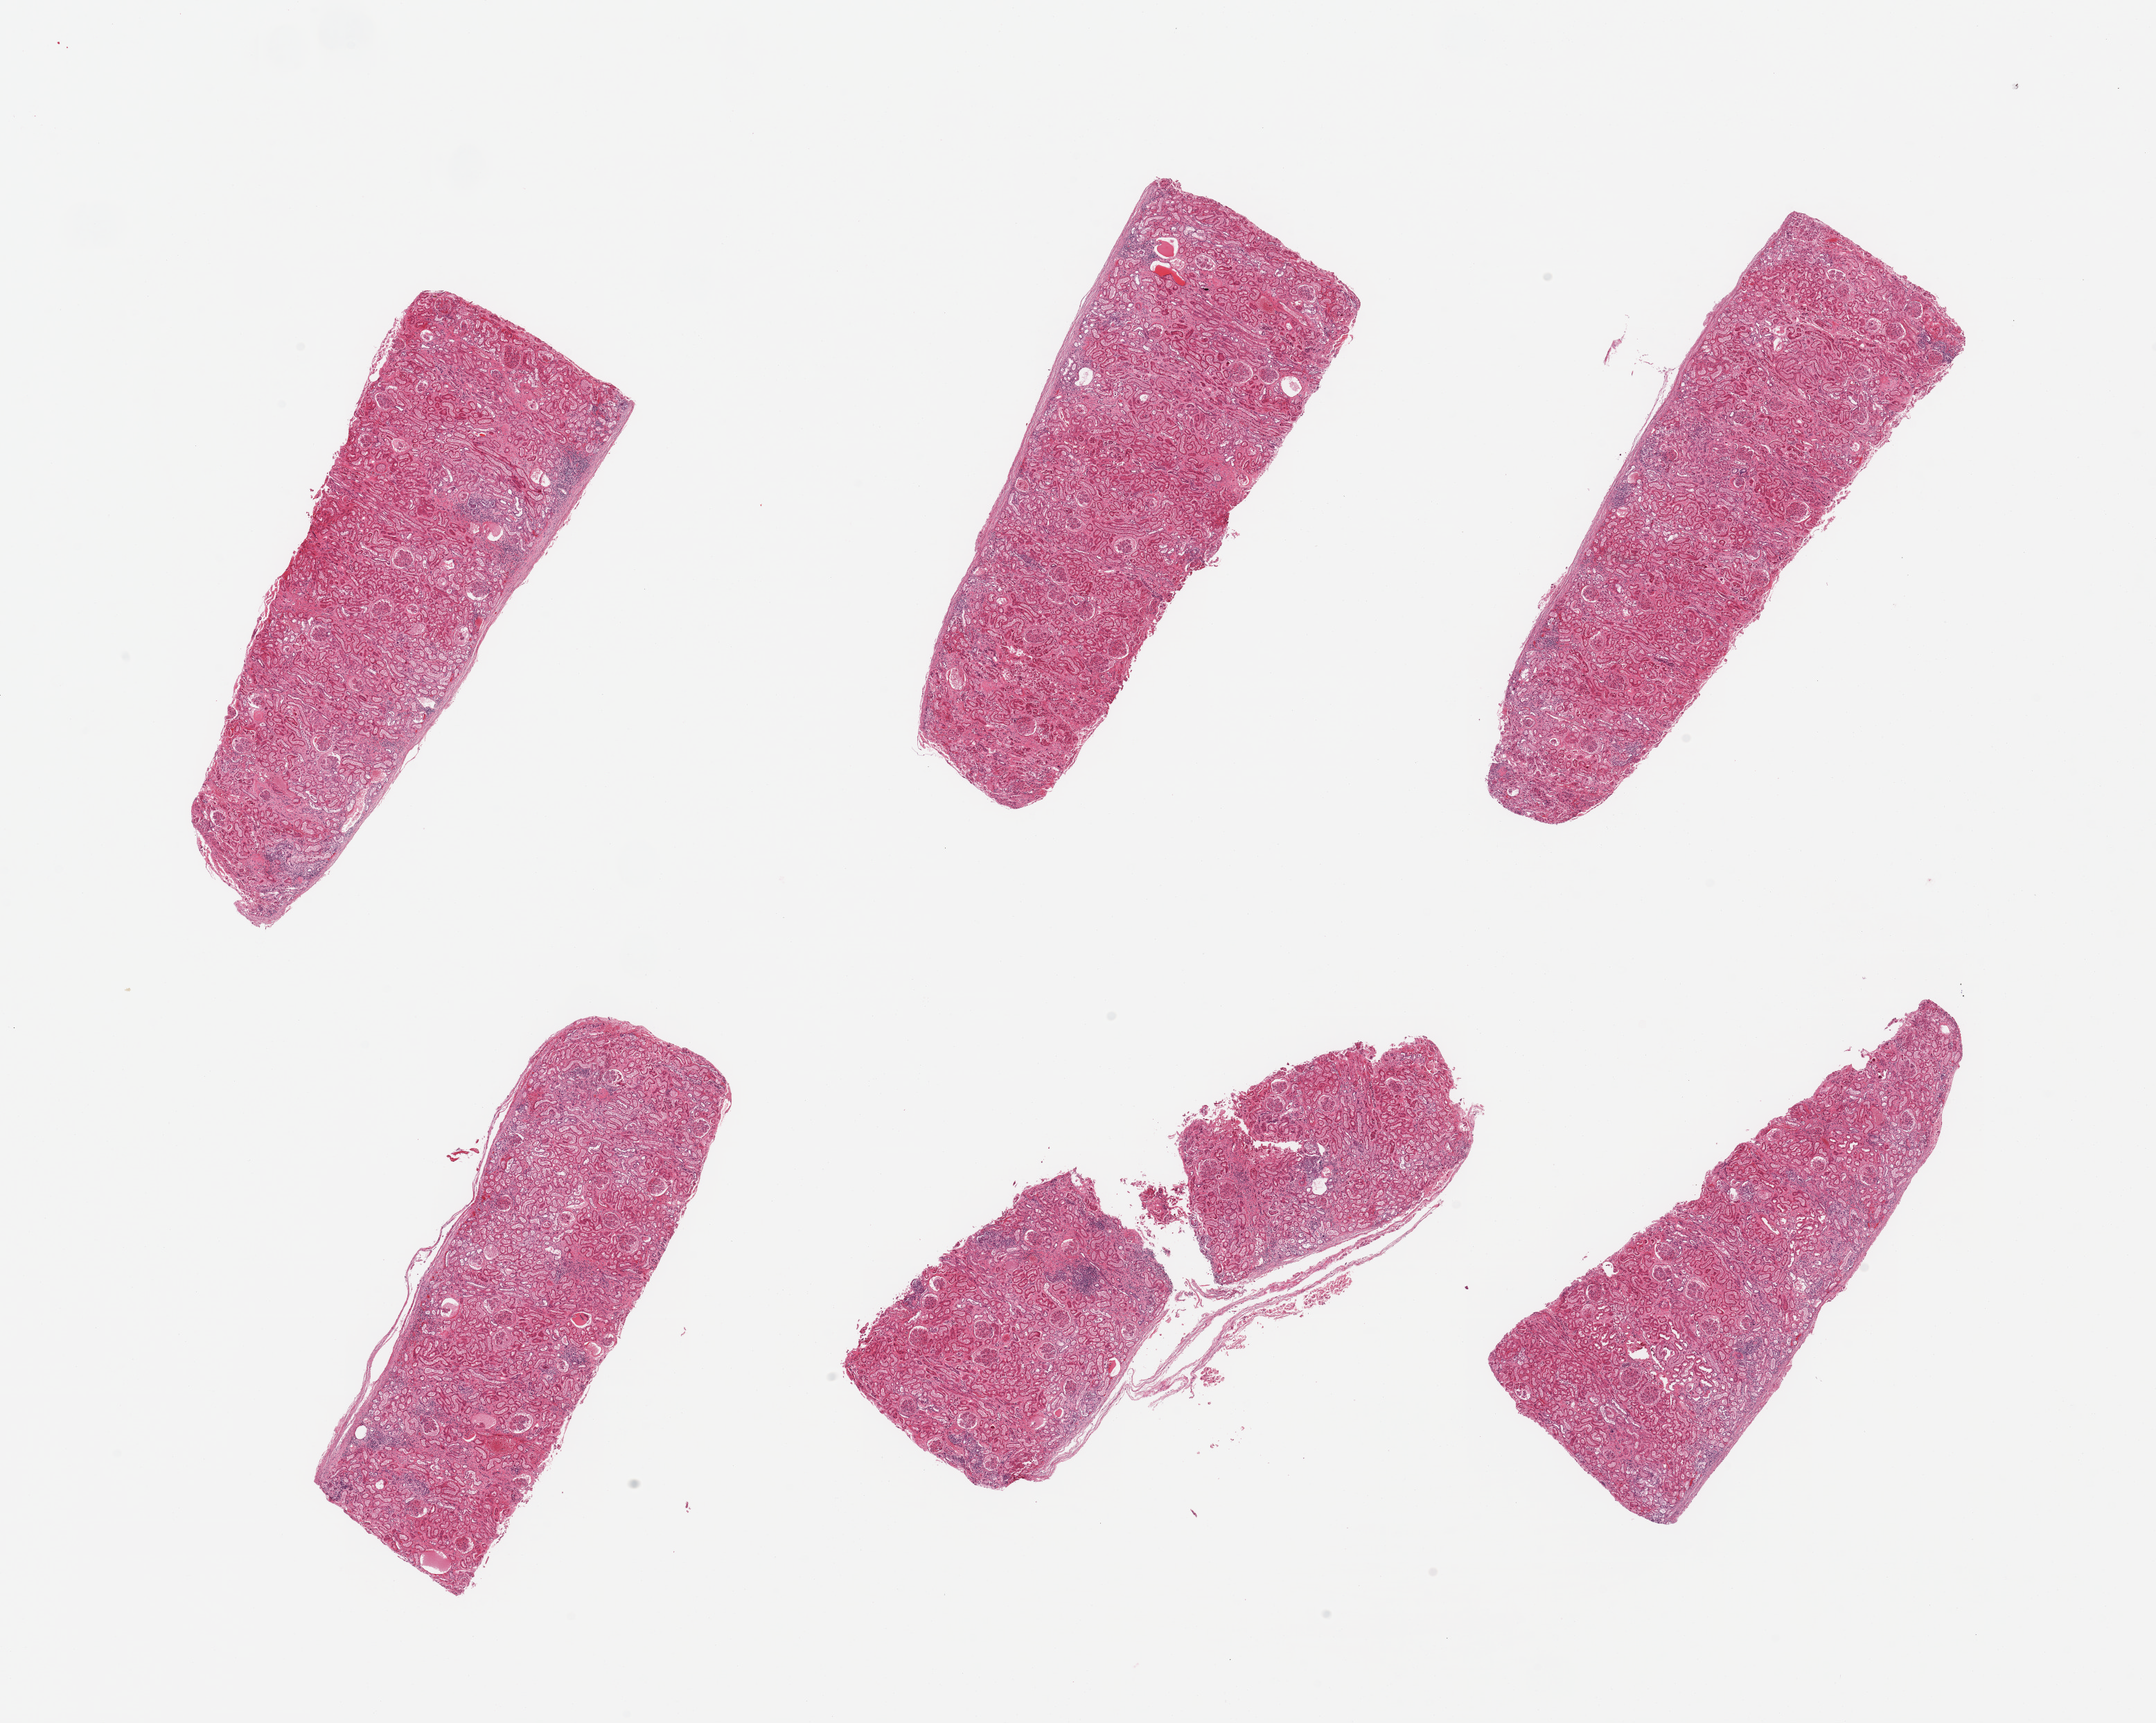
Whole-slide image, hematoxylin and eosin (H&E) stain — a low-resolution overview of the entire scanned area, about 24.6 x 19.7 mm (slide scanned at 20x). PAXgene-fixed, paraffin-embedded tissue. Sampled site (target tissue): renal cortex. Tissue donor sample. Male donor.
* pathologist's review note for this sample: 6 pieces; scattered small foci of chronic inflammation; no major vascular or glomerular lesions